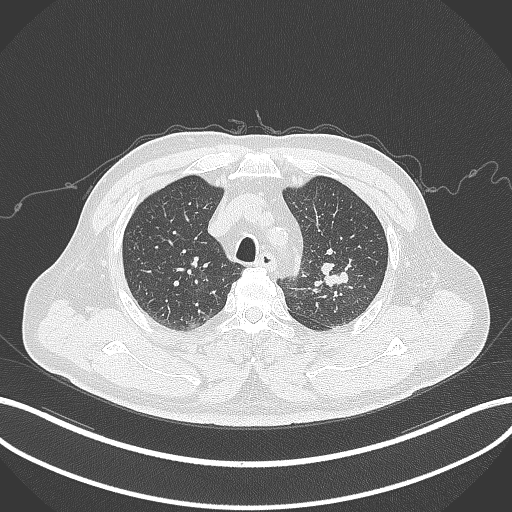
Chest CT, one axial slice. Position 239 of 286 along the scan axis. Reconstruction kernel B70f. Lung window (W 1500 / L -600 HU). 512 × 512 image matrix, field of view 400 × 400 mm. Male patient, age 67 years. Case-level facts recorded for this patient, not image findings: clinical TNM (as recorded): T2a N1 M0.
Annotated regions visible in this slice (rectangle marked by the reading radiologist):
- lung tumour (recorded histology: adenocarcinoma): bounding box (x1, y1, x2, y2) in pixels: (319, 257, 352, 287)